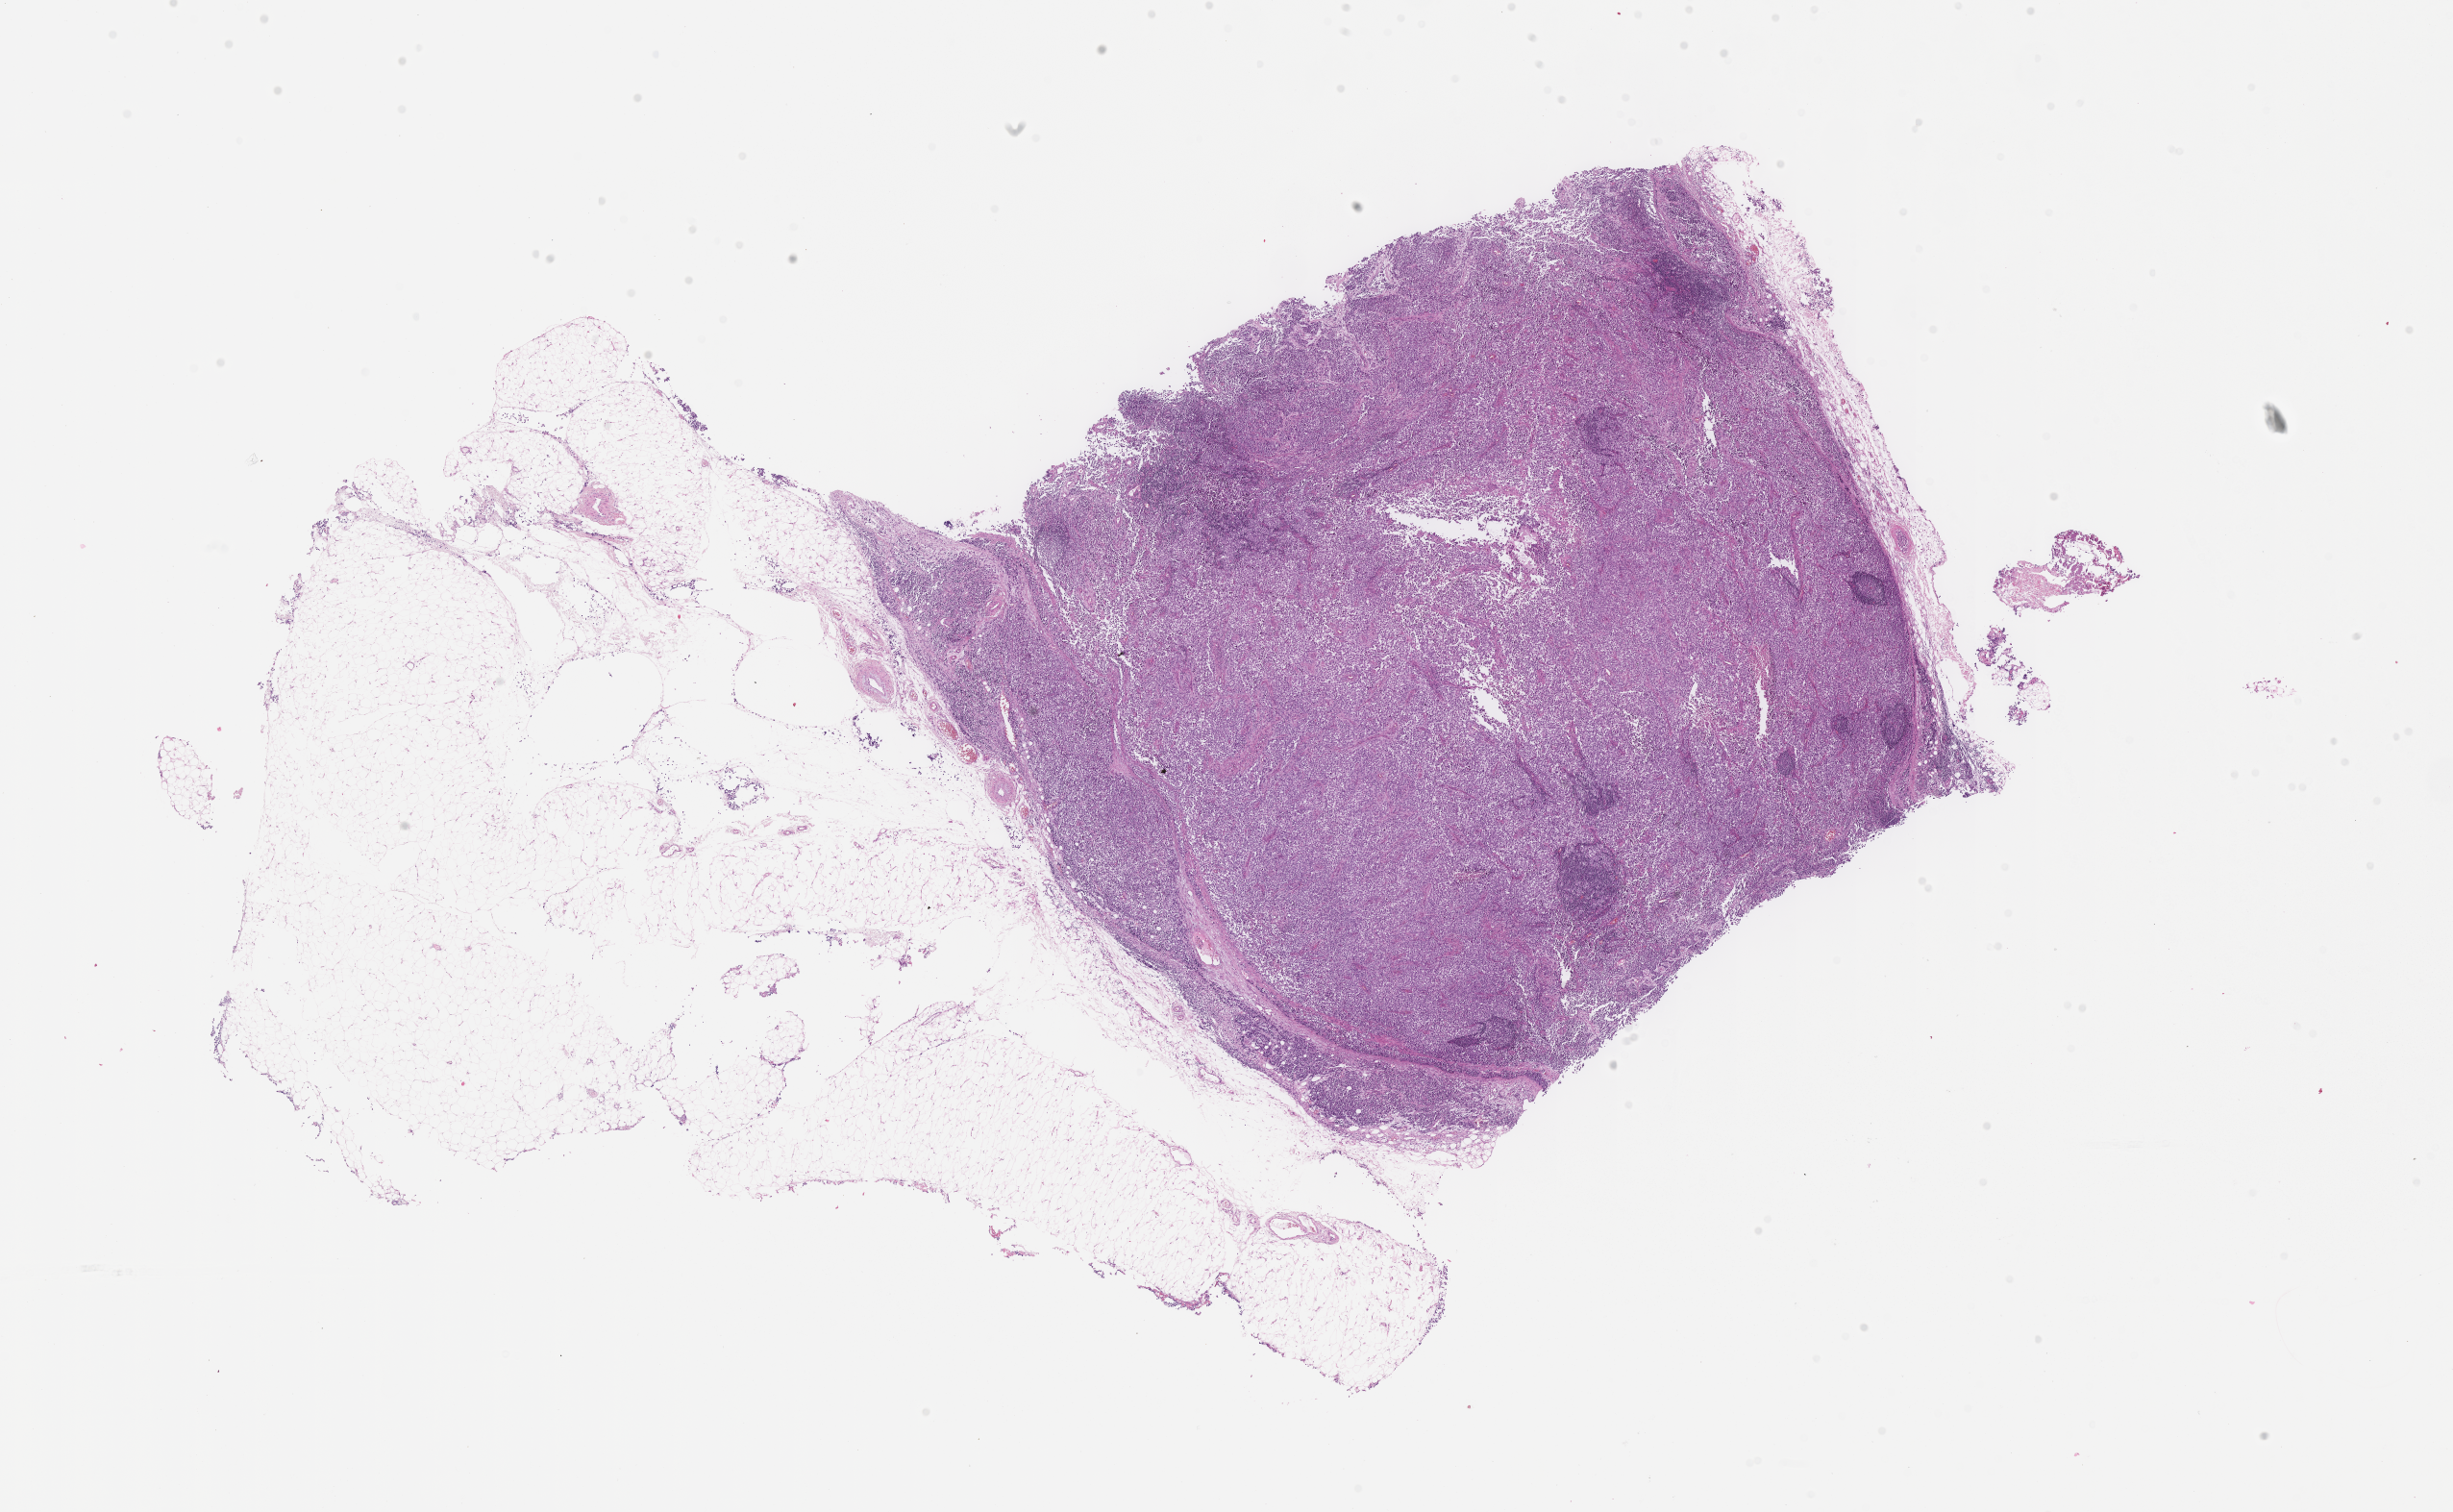
H&E whole-slide image of tumor tissue, whole scanned area (about 20.6 x 12.7 mm) shown as a low-resolution overview; formalin-fixed, paraffin-embedded (FFPE) tissue; sample anatomic site: peri-rectal mass. Patient: male, age 17.9 years at diagnosis.
Diagnosis: rhabdomyosarcoma; histological classification: alveolar rhabdomyosarcoma. Primary site (case record): prostate. Stage (as recorded): 3.